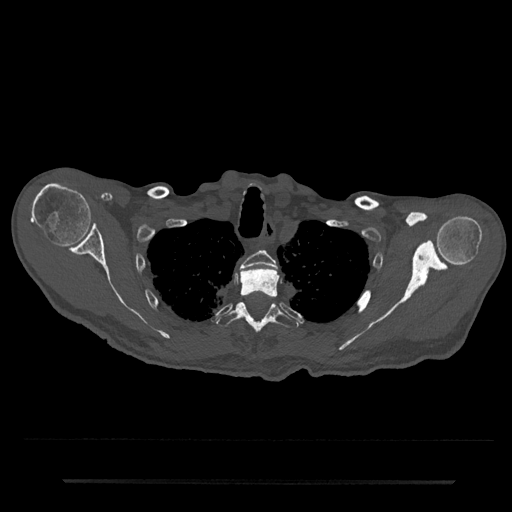
CT including the spine, one axial slice; slice 647 of 797 in the series (ordered by position); reconstruction kernel Br40s/3; 120 kVp; bone window (W 1800 / L 400 HU); 0.5 mm slice thickness; 512 × 512 image matrix, field of view 427 × 427 mm. Male patient, age 74 years. Case-level facts recorded for this patient, not image findings: primary cancer: prostate.
Outlined on this slice (semi-automatic segmentation, software-assisted and operator-edited):
- T2 vertebra: bounding box <241,250,277,269> (left, top, right, bottom; pixels)
- T3 vertebra: <240,267,278,298>
- T4 vertebra: <216,302,299,335>